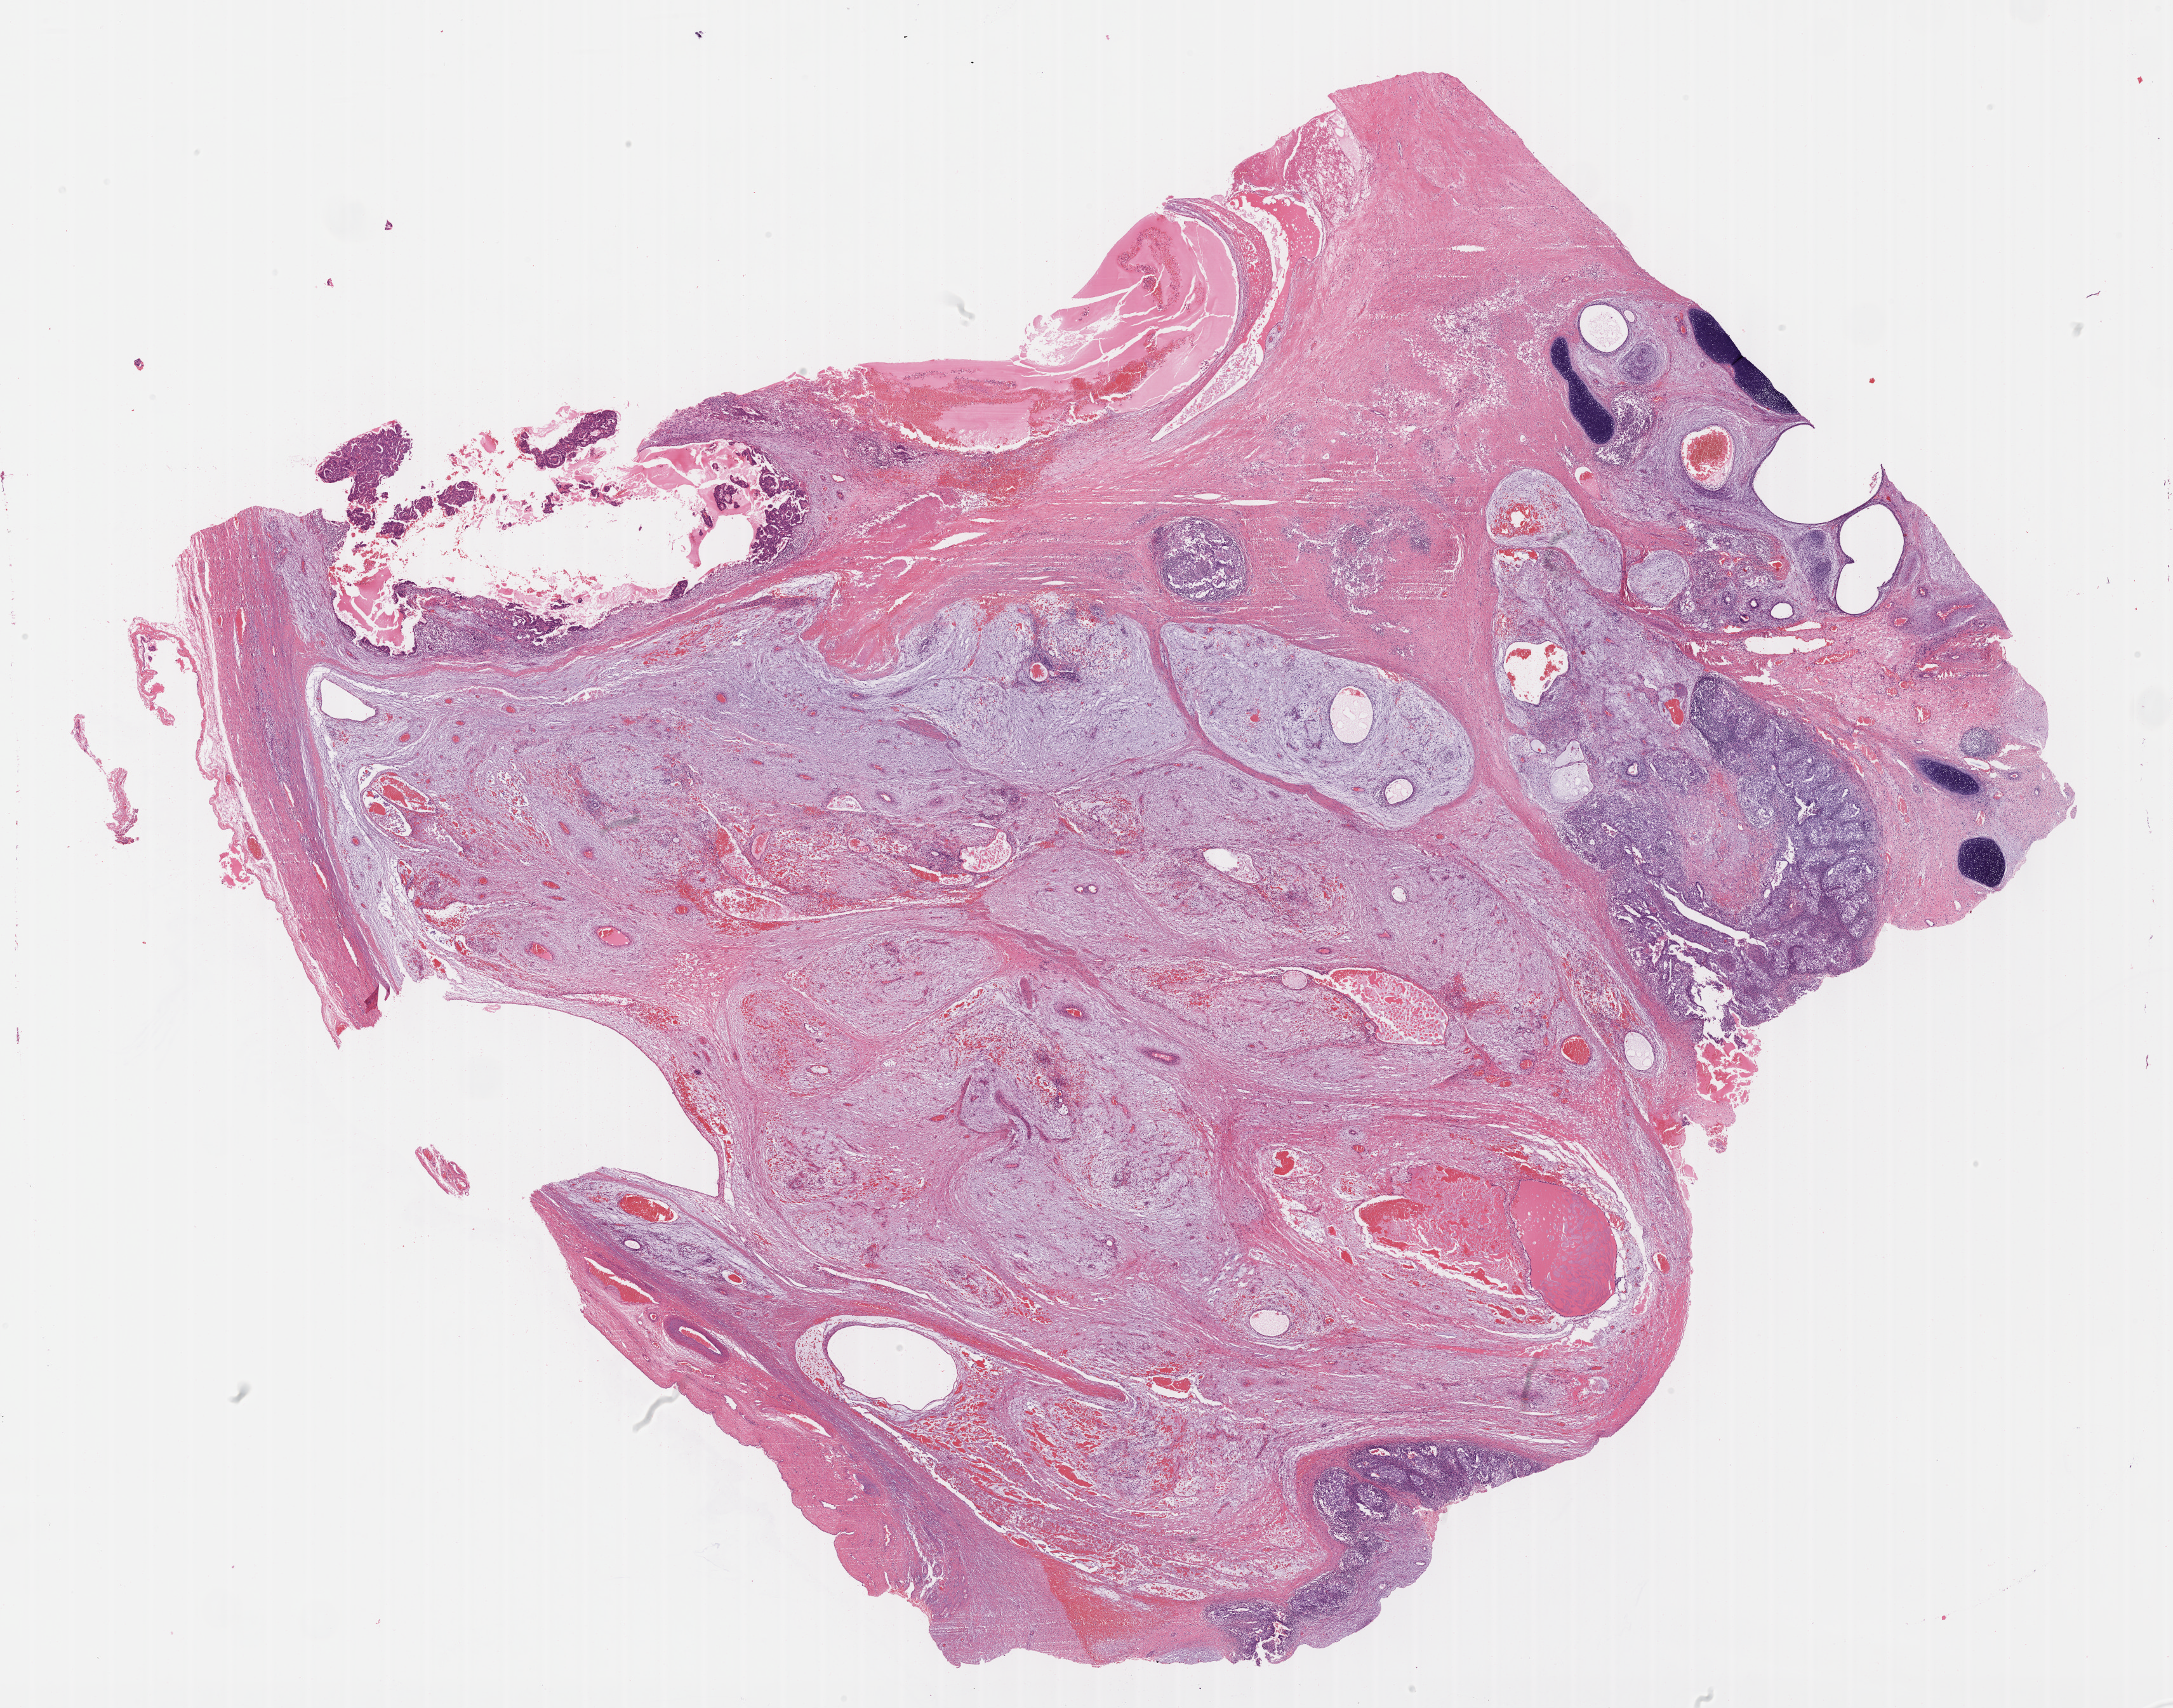
Digitized H&E-stained tissue section (whole slide), low-resolution overview of the scanned area, about 27.7 x 21.7 mm (acquisition: 40x scan), formalin-fixed paraffin-embedded (FFPE) diagnostic section, testis, primary tumour sample. Patient: male, age at initial diagnosis 27 years.
AJCC pathologic stage: IS (6th edition). Diagnosis: Teratocarcinoma. TNM: T1 NX M0.